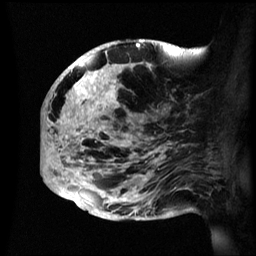
Breast MRI (dynamic contrast-enhanced), one sagittal slice; position 25 of 60 along the scan axis; dynamic contrast-enhanced series, image 2 of 3 at this slice position (ordered by acquisition); 1.5 T; TE 4.2 ms, TR 8.4 ms; 2.4 mm slice thickness; 256 × 256 image matrix. Patient: female, 48 years.
Annotated regions visible in this slice (semi-automatic segmentation, software-assisted and operator-edited):
- analysis volume of interest (the breast-tissue region the enhancement analysis was run in; not a lesion): bounding box <42,41,195,221> (left, top, right, bottom; pixels)
- tumour enhancement mask (voxels above the 70 % enhancement threshold inside the analysis volume of interest): <43,41,178,219>